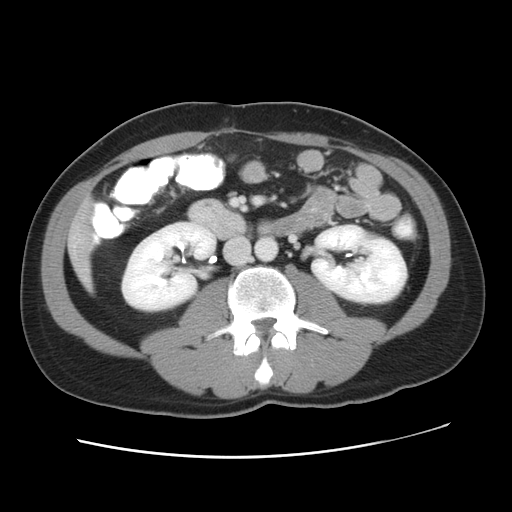
Contrast-enhanced abdominal CT, one axial slice. Slice 15 of 49 in the series (ordered by position). Reconstruction kernel STANDARD. Intravenous contrast given. Soft-tissue window (W 400 / L 40 HU). 512 × 512 image matrix, field of view 363 × 363 mm. Male patient, age 41 years. From the clinical record (not read from this slice): diagnosis: colorectal cancer liver metastases, imaged before liver resection; multiple liver metastases: yes; largest metastasis: 0.7 cm; chemotherapy before resection: yes.
Annotated regions visible in this slice (expert manual segmentation):
- liver: bounding box [x1, y1, x2, y2] px = [69, 205, 92, 287]